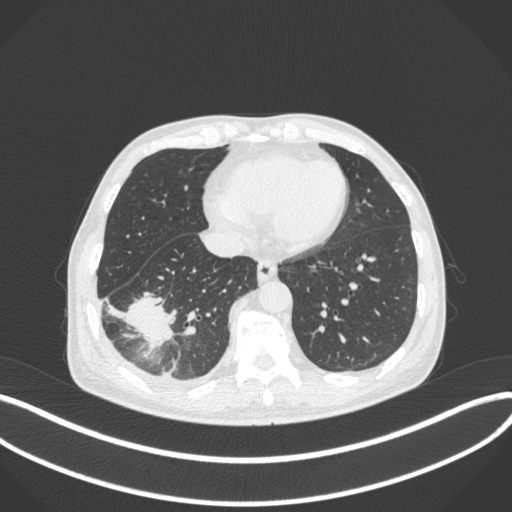
Chest CT, one axial slice. Position 113 of 385 along the scan axis. 120 kVp. Lung window (W 1500 / L -600 HU). 512 × 512 image matrix, field of view 400 × 400 mm. Male patient, age 64 years. From the clinical record (not read from this slice): clinical TNM (as recorded): T3 N0 M0.
Outlined on this slice (rectangle marked by the reading radiologist):
- lung tumour (recorded histology: adenocarcinoma): bounding box (x1, y1, x2, y2) in pixels: (126, 291, 180, 355)